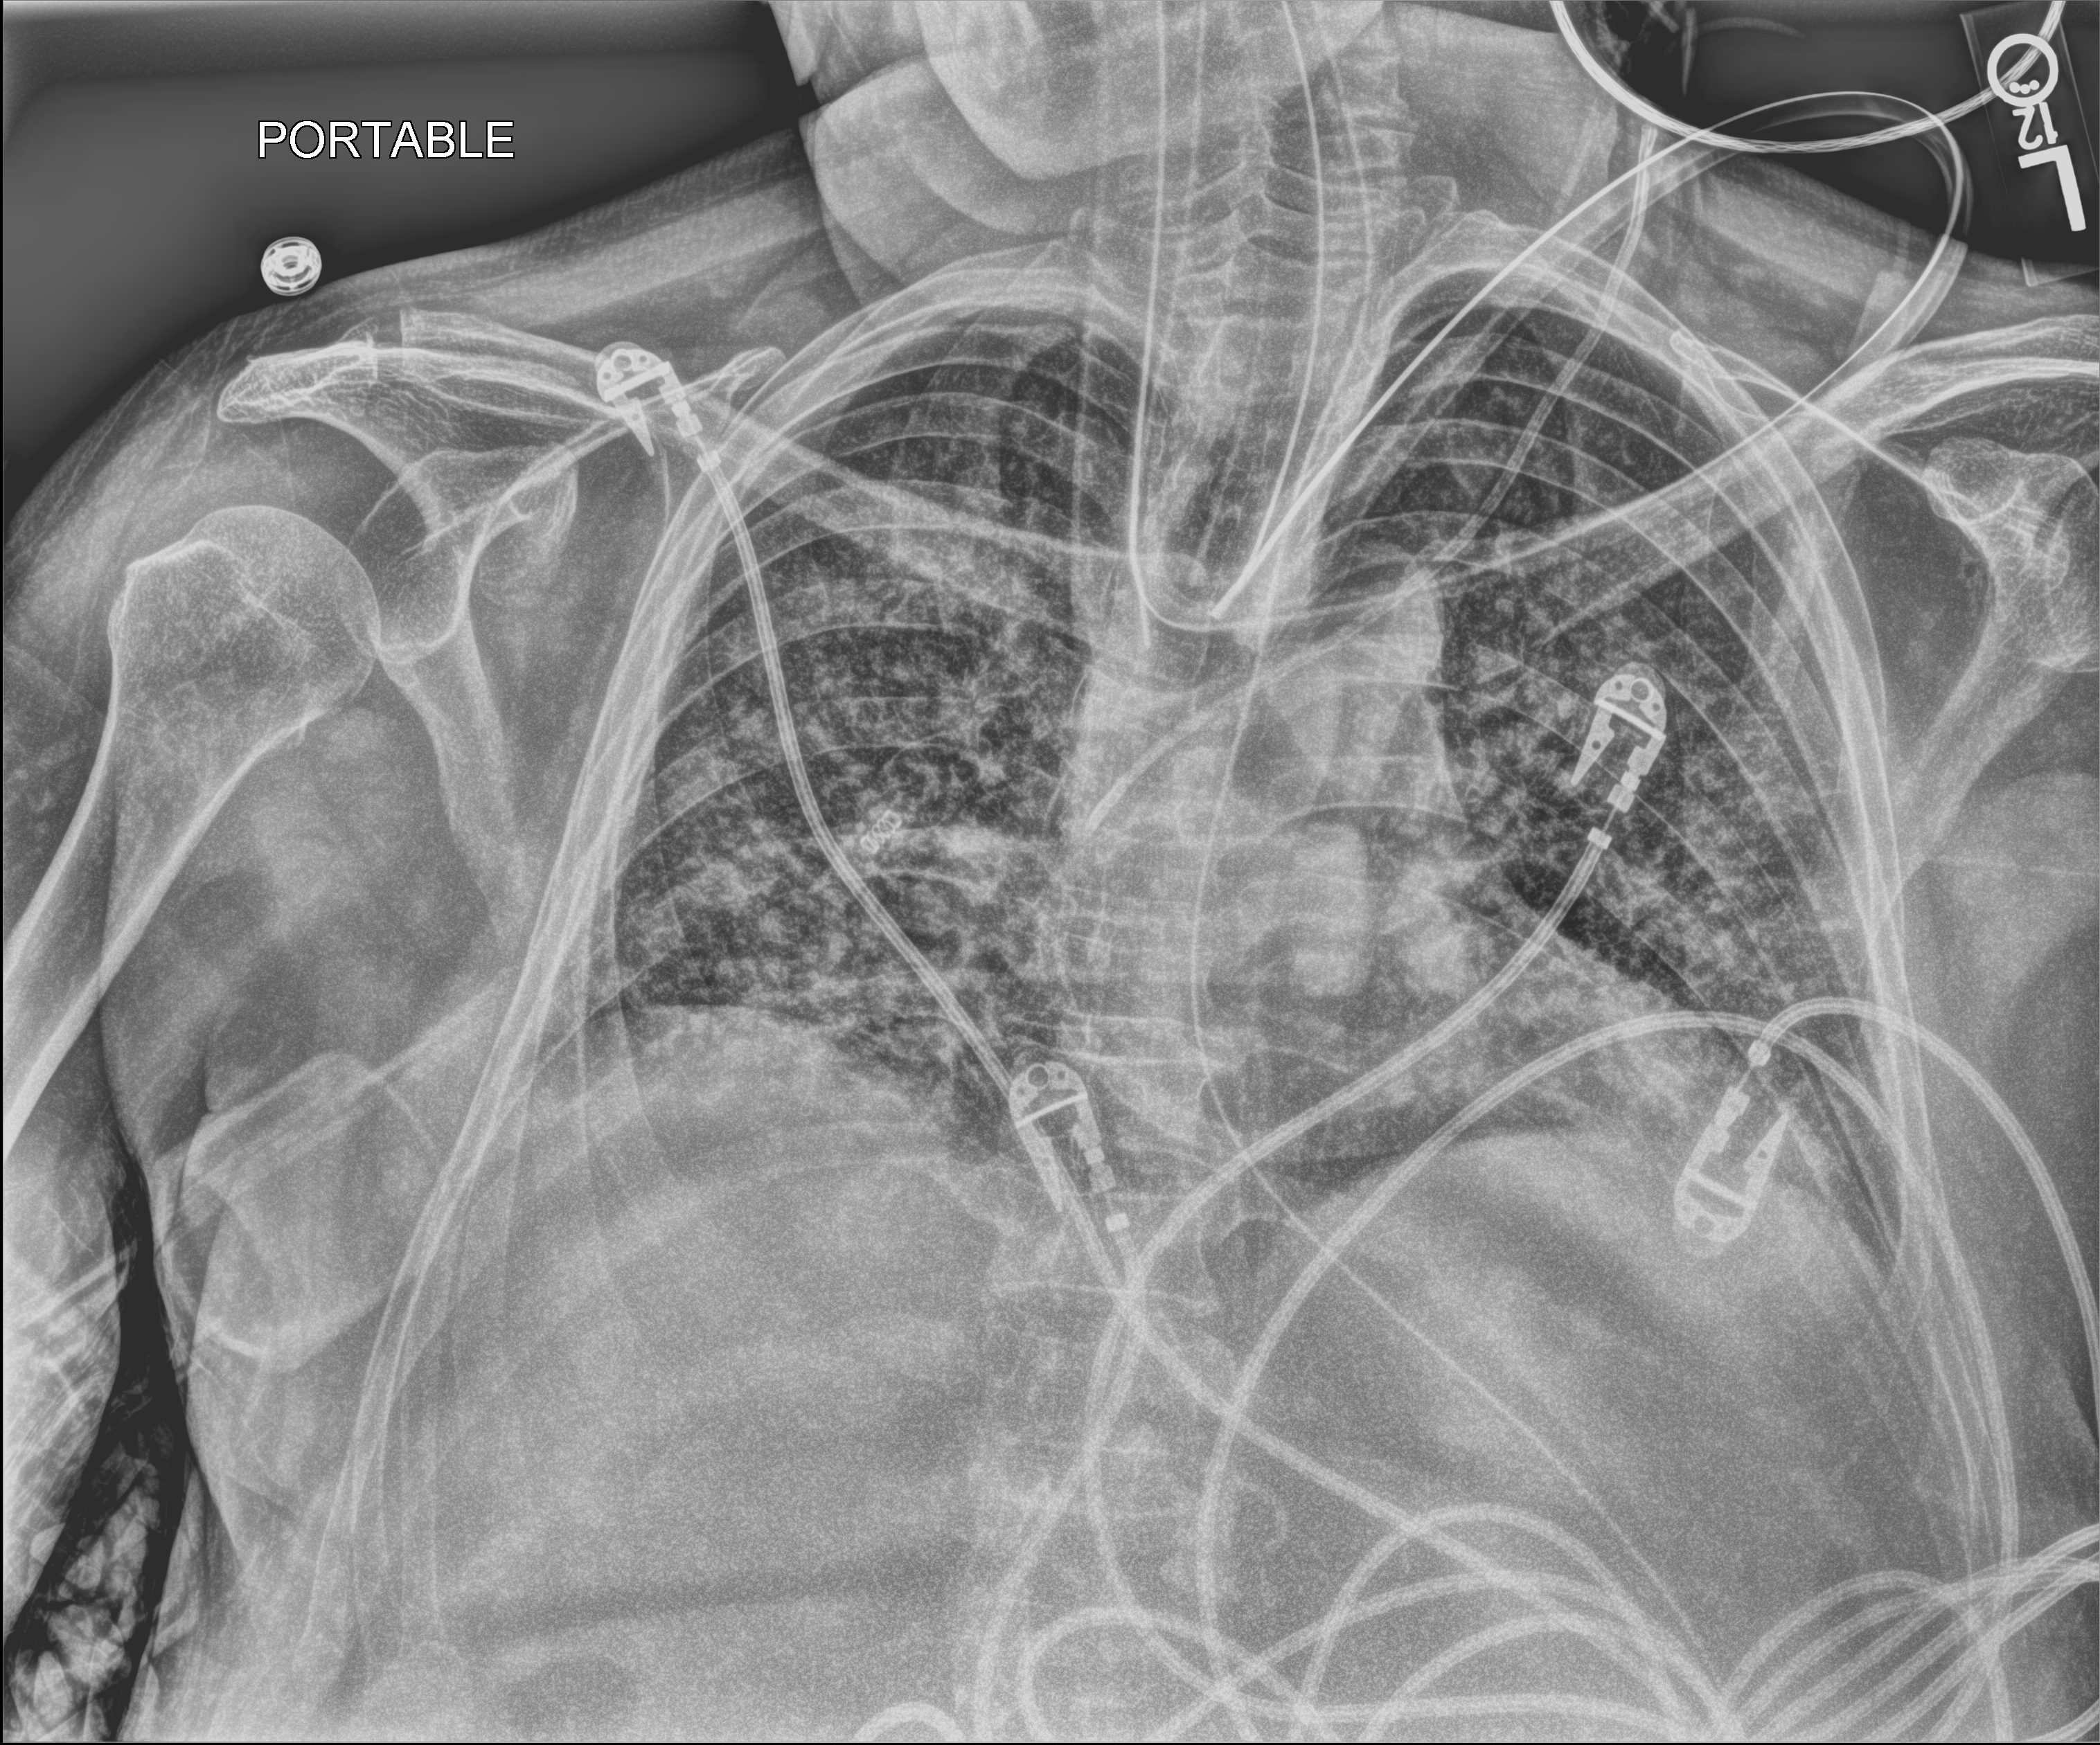
Chest X-ray (portable); anteroposterior (AP) projection. Male patient hospitalised with COVID-19, age 60–74 years.
Hospital-stay facts (about this admission, not read from this image; timing relative to this image not recorded):
- admitted to intensive care during this hospital stay: yes
- smoking status (admission record): never
- mechanically ventilated during this hospital stay: yes